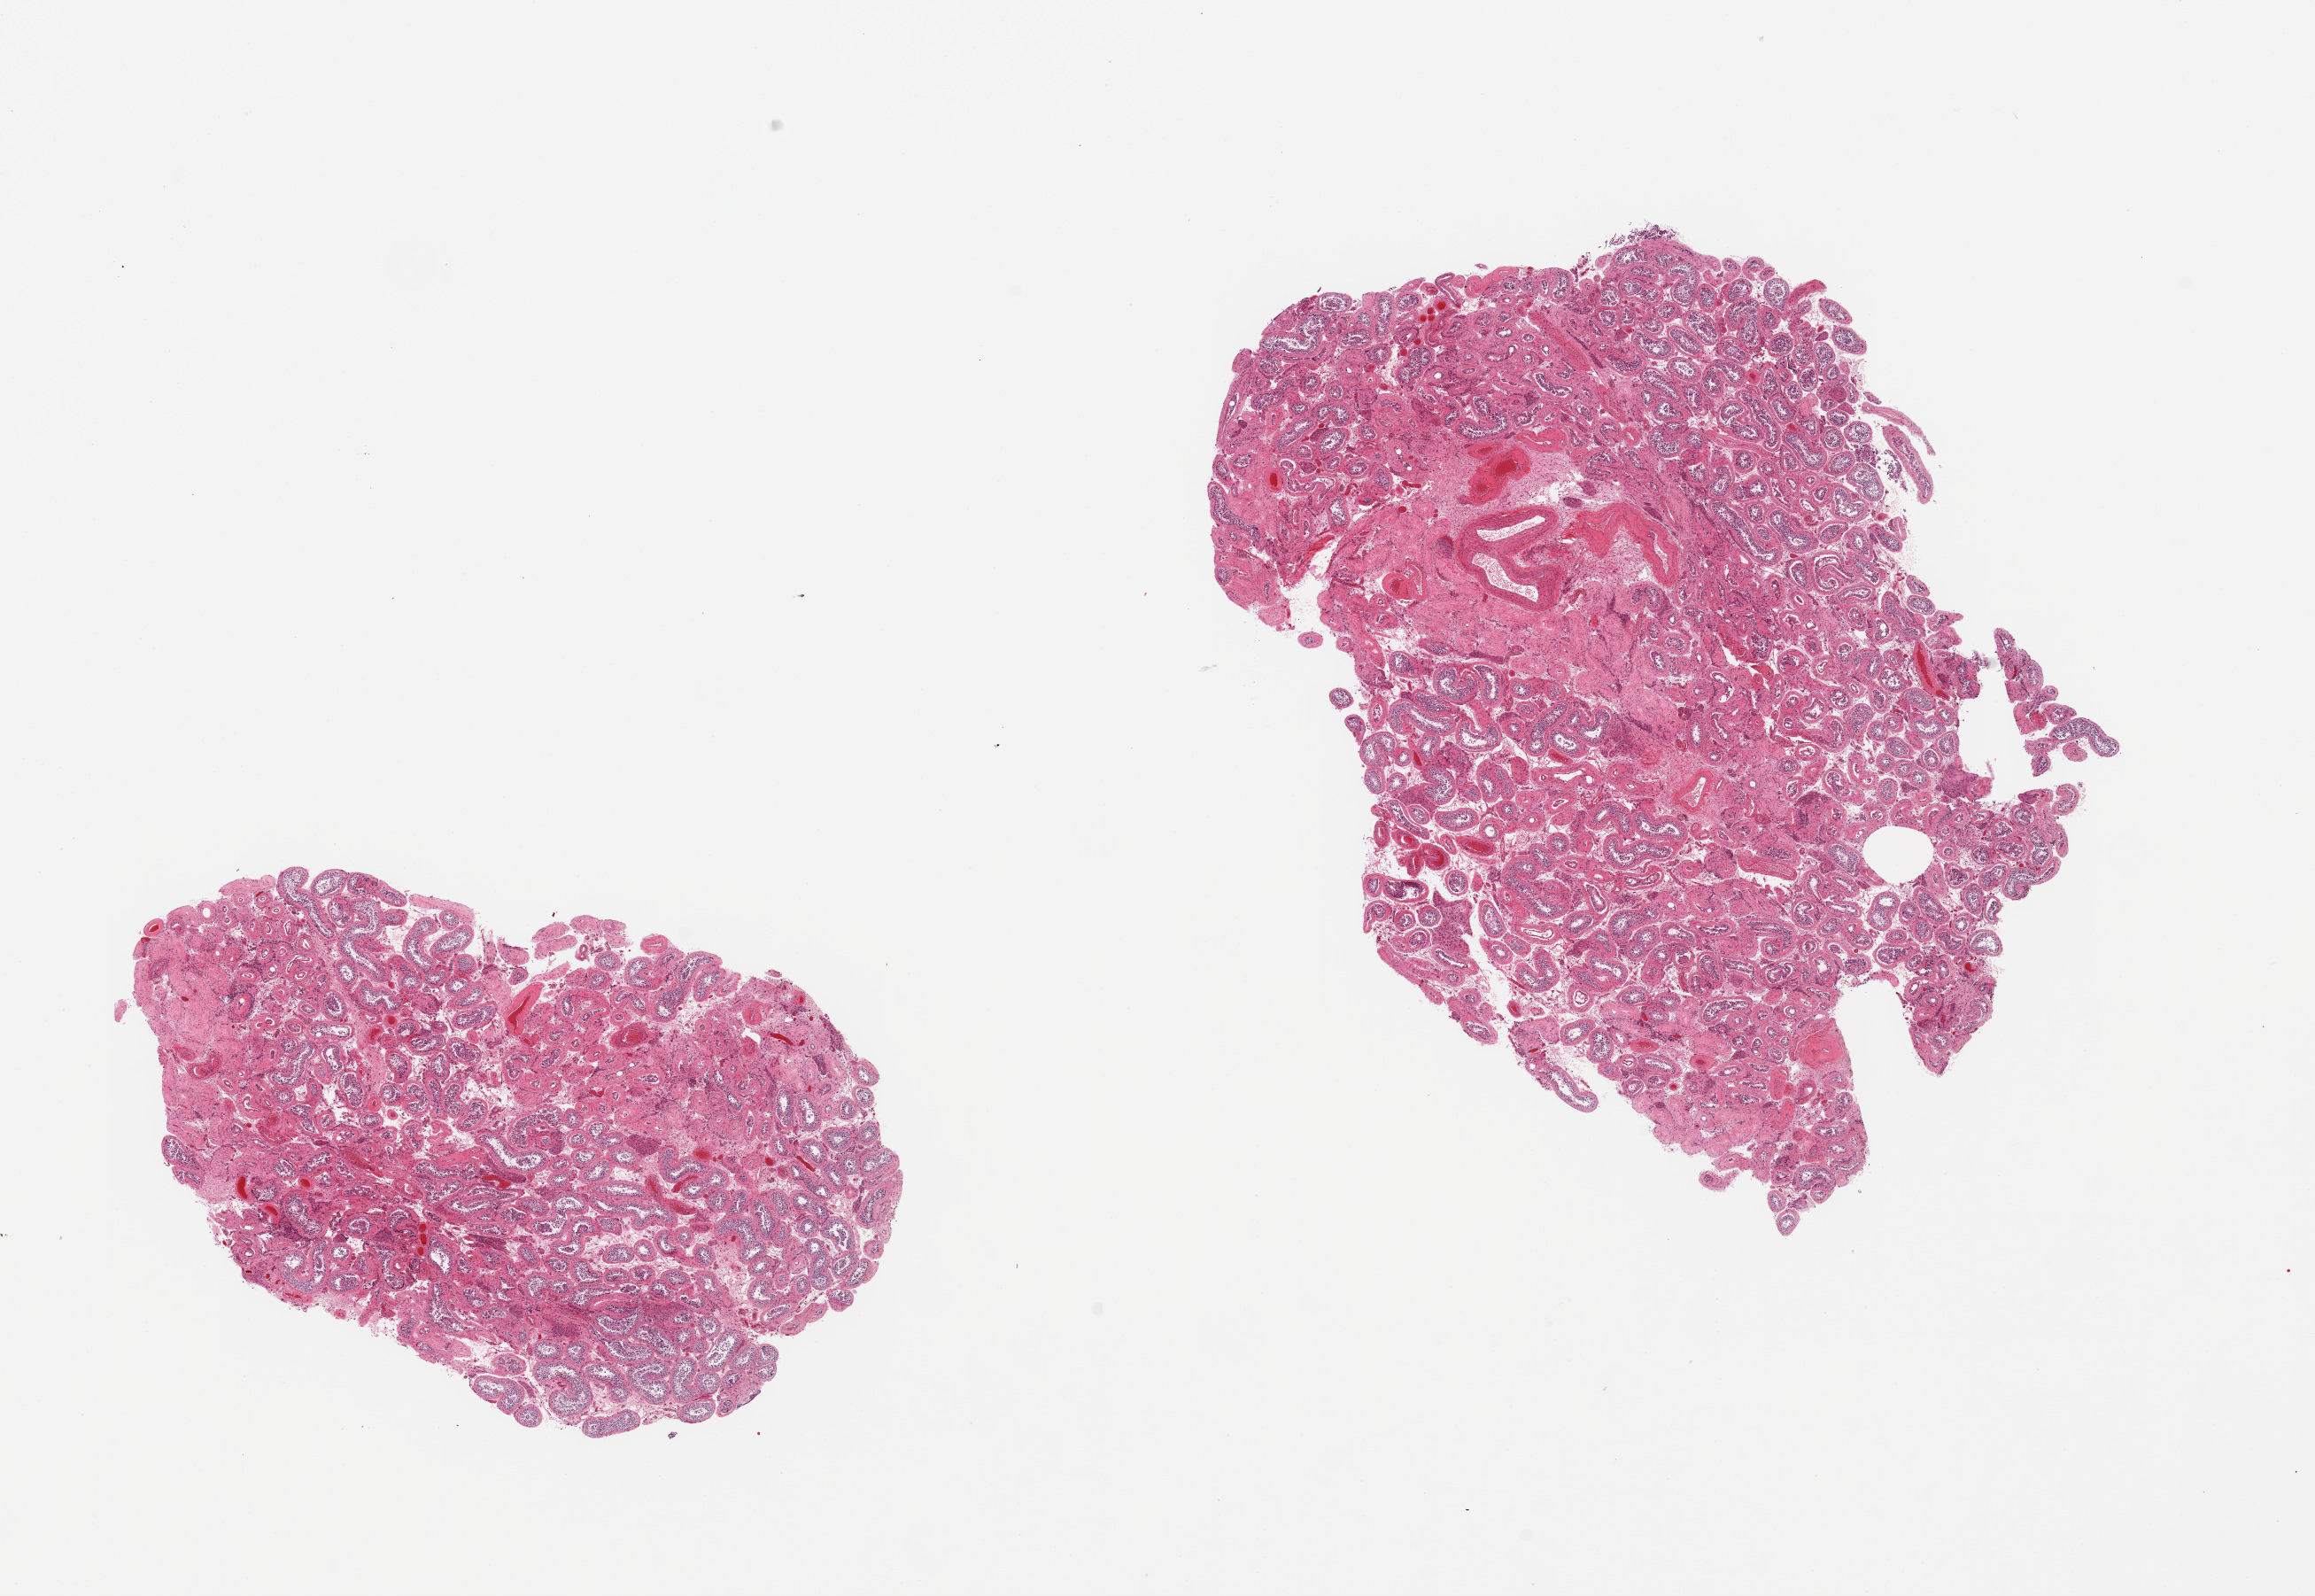
Digitized H&E-stained section, brightfield, whole scanned area (about 20.7 x 14.3 mm) shown as a low-resolution overview, PAXgene-fixed, paraffin-embedded tissue, sampled site (target tissue): testis, donor tissue sample. Male donor.
Reviewer comment on this tissue sample: 2 pieces; spermatogenesis noted; increased peritubular fibrosis and focal hyalinization.